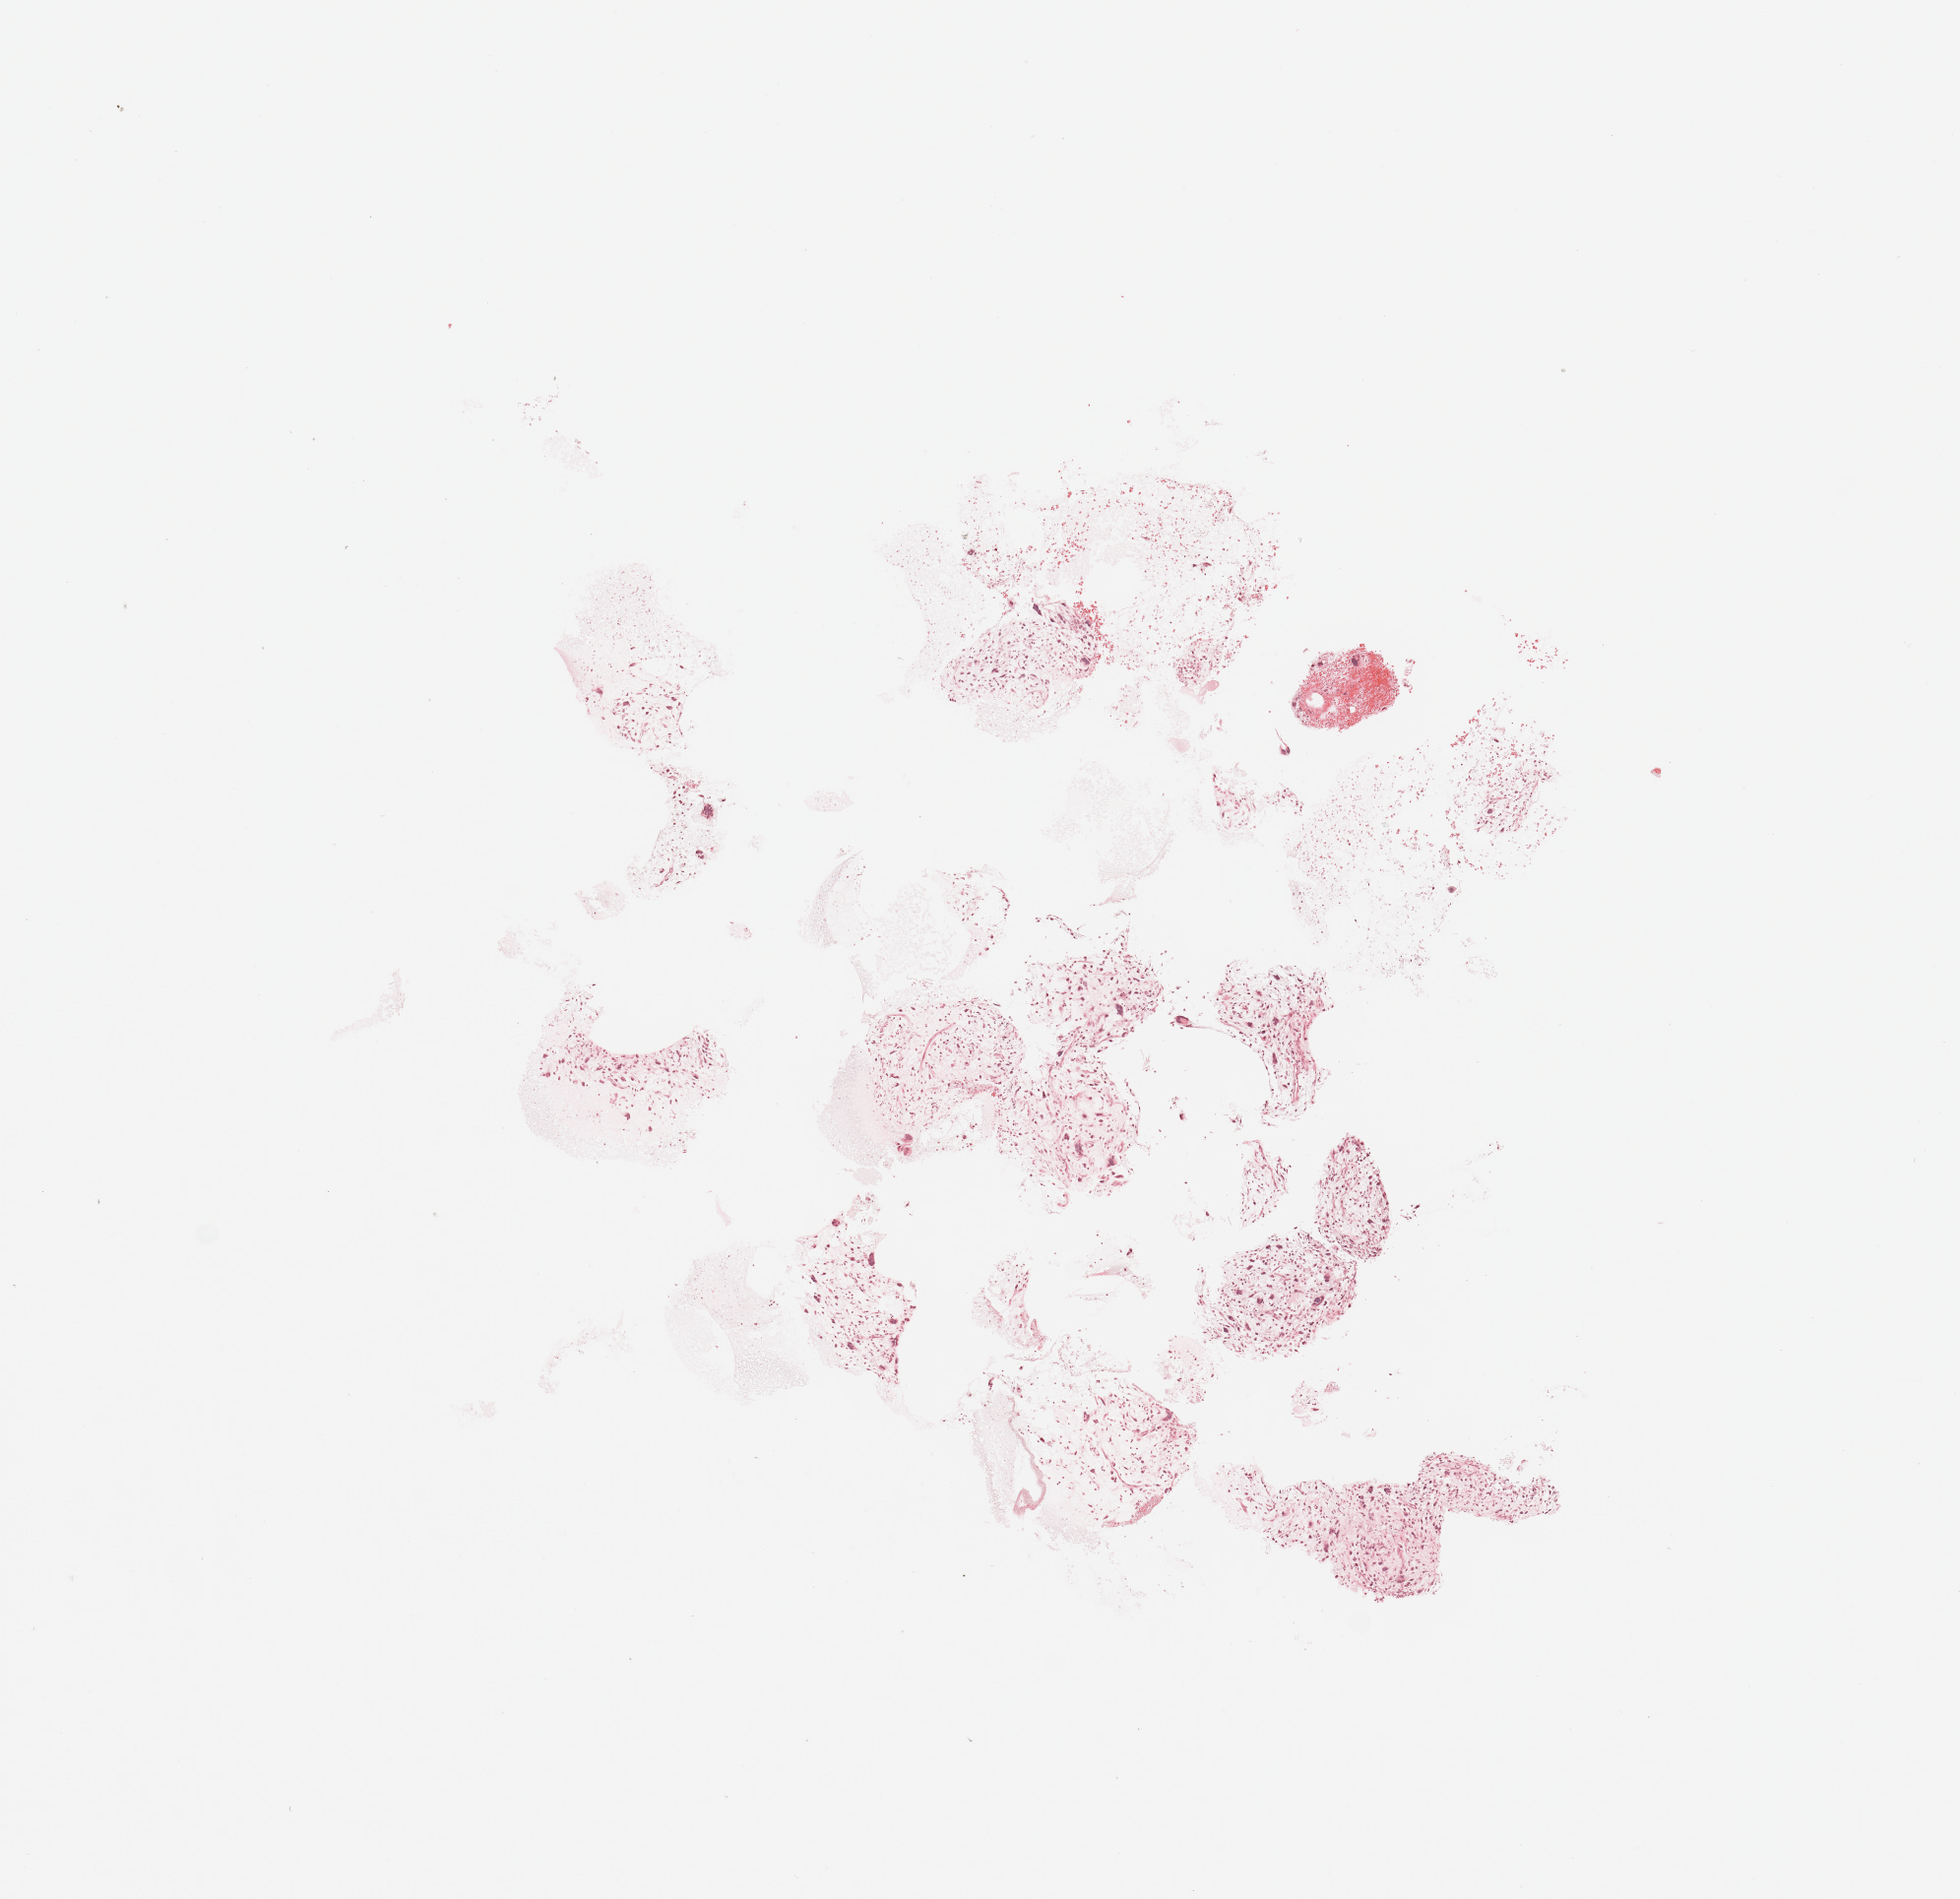
H&E whole-slide image, shown as a low-resolution overview of the whole scanned area (about 7.9 x 7.6 mm, from a 20x scan); tumour tissue sample. Female, 51 y/o.
Primary tumour site (as recorded): lower extremity. Patient diagnosis (cohort enrolment): sarcoma (site not recorded at cohort level).